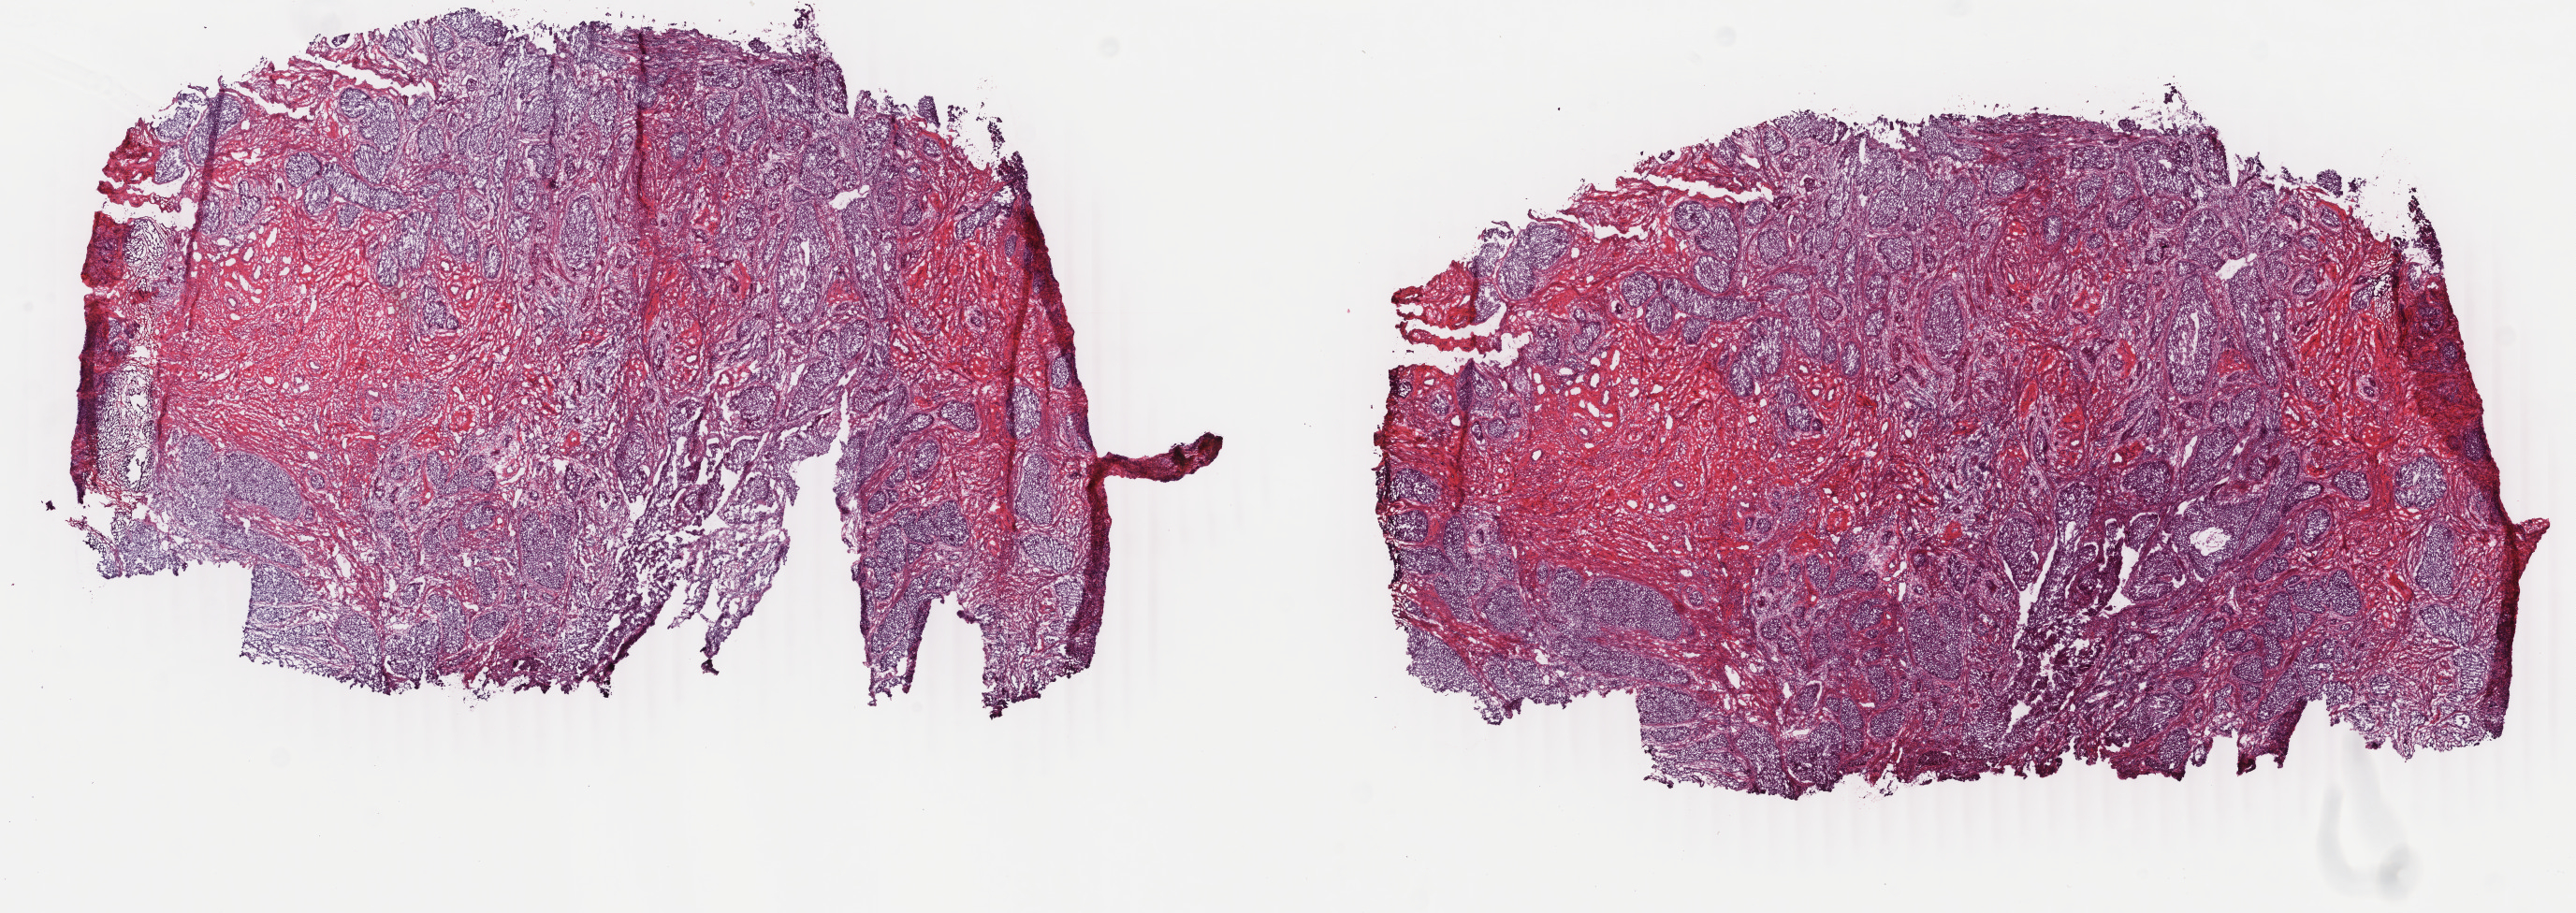
Hematoxylin and eosin (H&E) stained whole-slide image, shown as a low-resolution overview of the whole scanned area (about 21.9 x 7.8 mm), frozen section, cervix, primary tumour sample. Patient: female, age at initial diagnosis 45 years. Histologic grade: G3 (poorly differentiated). Composition of this section per pathologist review: tumour cells 50%, tumour nuclei 60%, normal cells 35%, stromal cells 10%, necrosis 5%. Inflammatory infiltration, as recorded: lymphocyte infiltration 12%, monocyte infiltration 0%, neutrophil infiltration 1%.
Pathologic diagnosis: Squamous cell carcinoma, NOS (cervix uteri). Lymph nodes positive (case pathology): 1 of 16 examined.